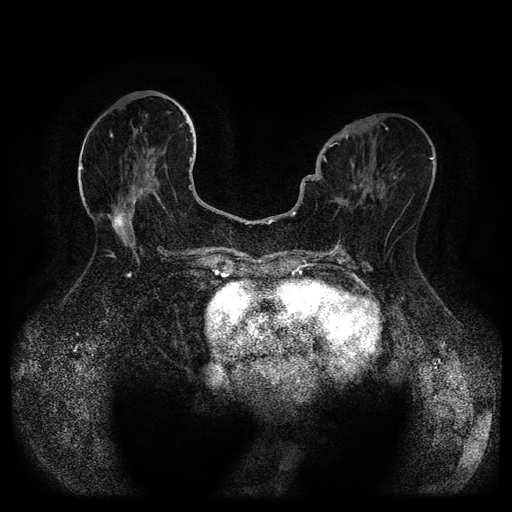
Breast MRI (dynamic contrast-enhanced, multi-phase), one axial slice; slice 42 of 116 in the series (ordered by position); dynamic contrast-enhanced series, time point 2 of 5 at this slice position (early post-contrast); 1.5 T; TE 2.6 ms, TR 5.3 ms; 2 mm slice thickness; 512 × 512 image matrix, field of view 350 × 350 mm. Patient: female, 75 years.
Structures marked on this image (semi-automatically segmented with operator editing):
- breast lesion (labelled benign in the annotation): bounding box [x1, y1, x2, y2] px = [107, 211, 125, 234]